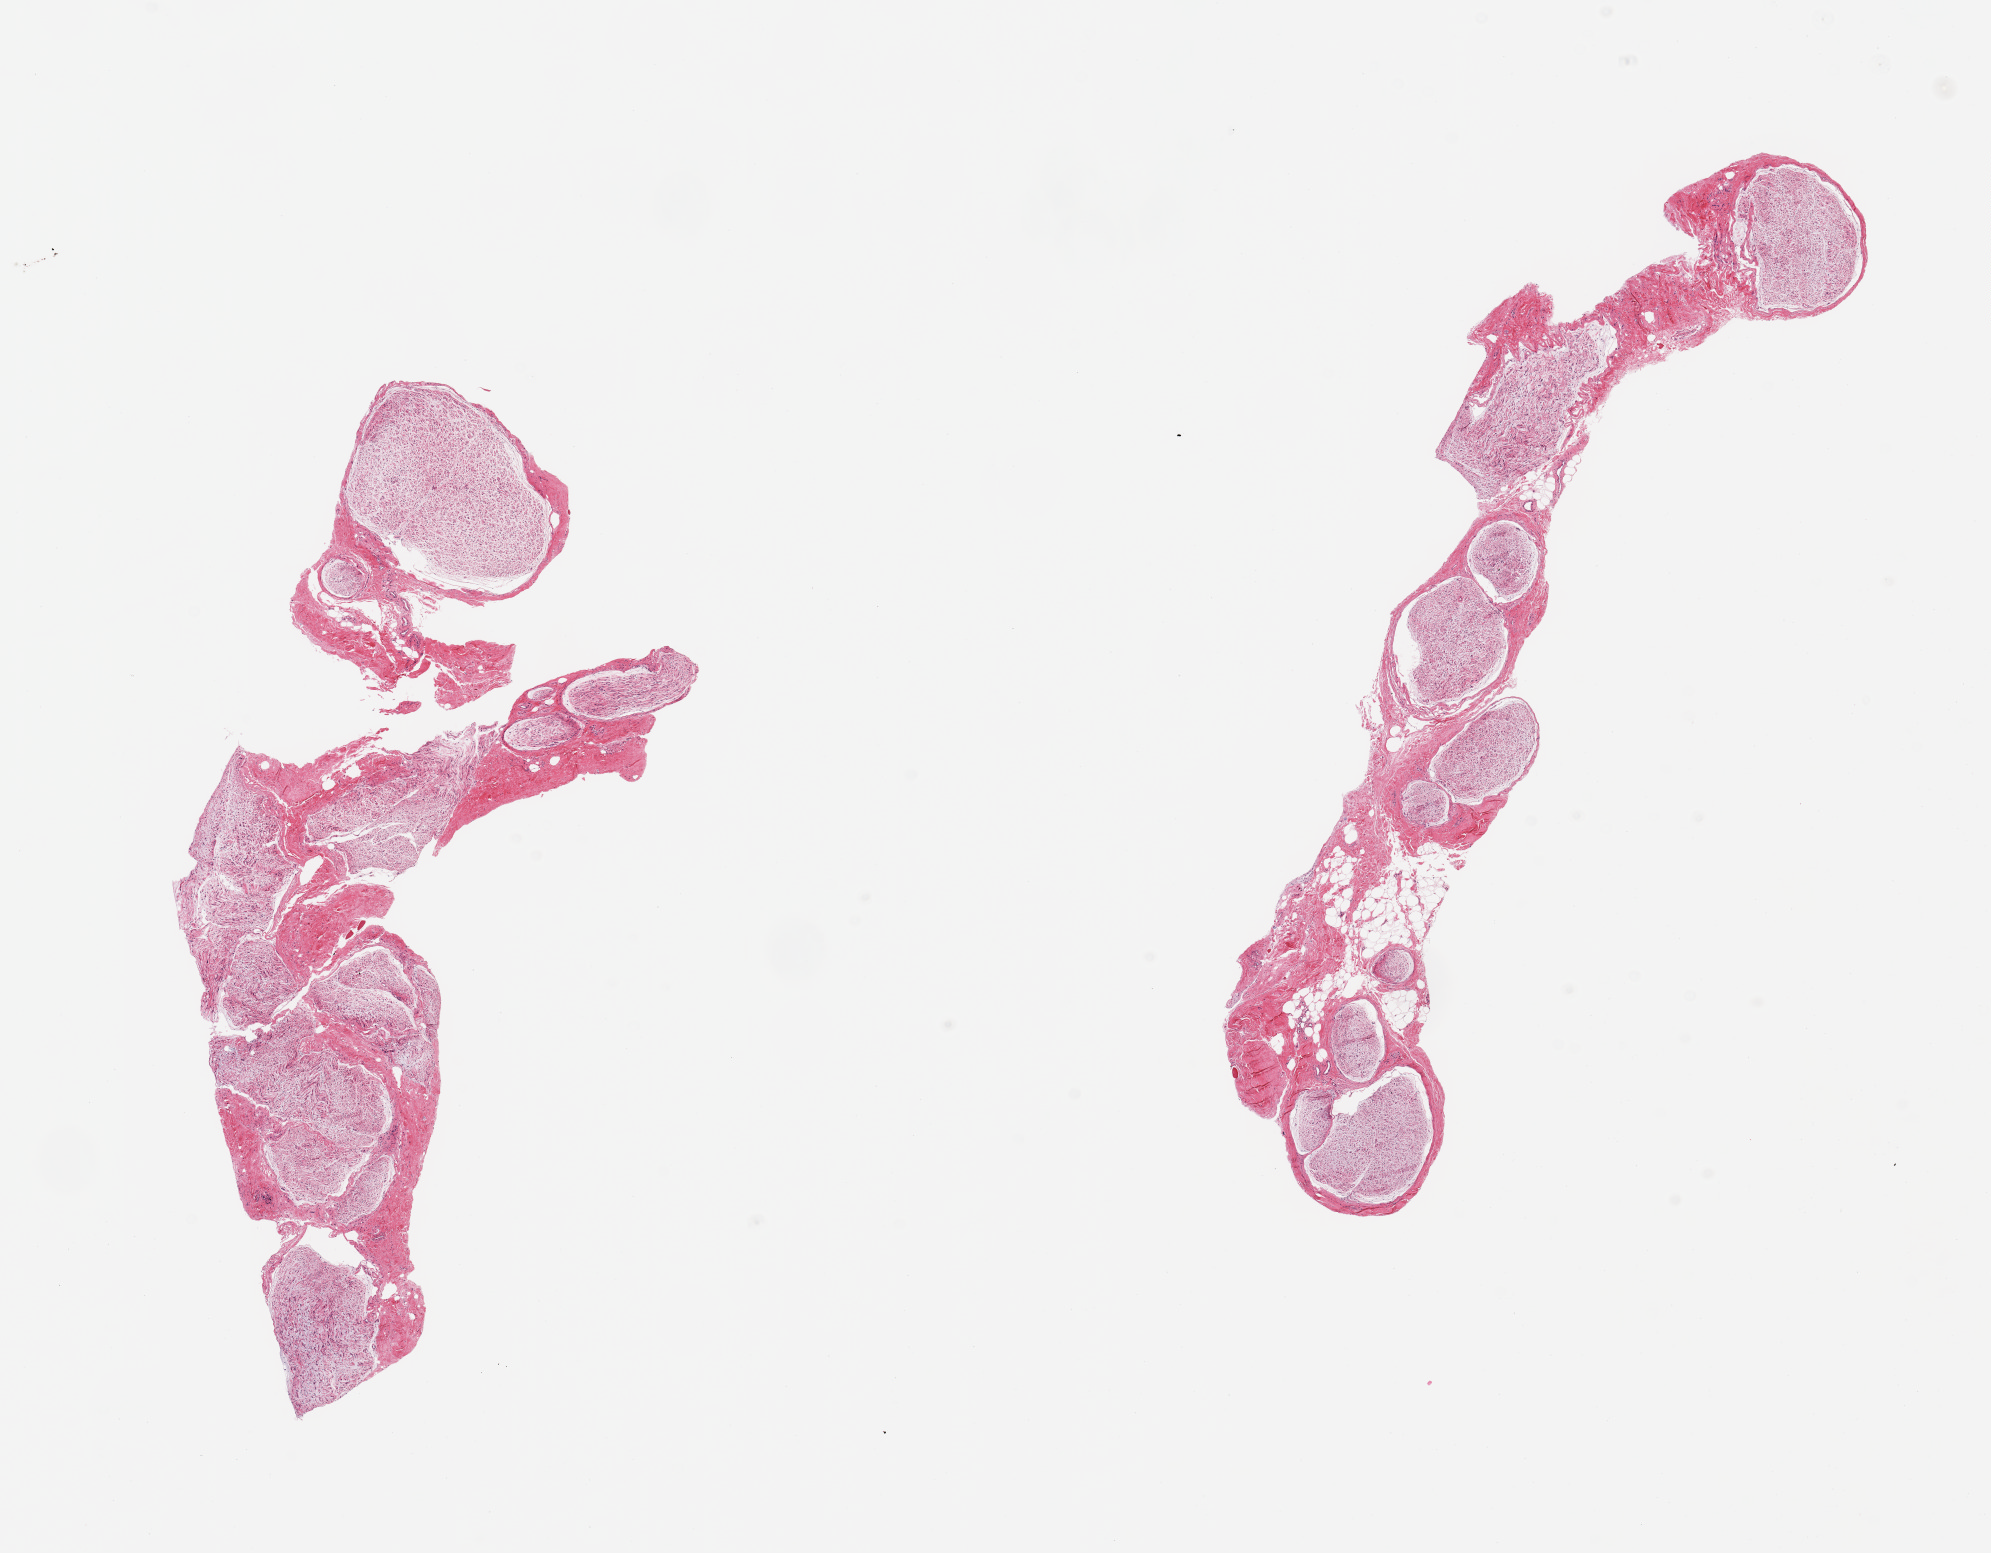
Digitized hematoxylin and eosin (H&E)-stained section, whole scanned area (about 15.8 x 12.3 mm, from a 20x scan) shown as a low-resolution overview; PAXgene-fixed, paraffin-embedded tissue; sampled site (target tissue): tibial nerve; donor tissue sample.
Review note (as recorded): 2 pieces; moderate atrophy; 20% internal fat in 1 piece.